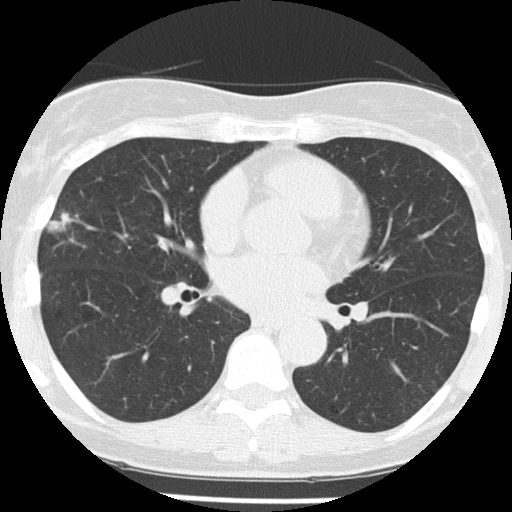
Low-dose screening chest CT, axial slice, first (baseline) screen, lung window (W 1500 / L -600 HU). Female participant, aged 58 years at enrolment. Former smoker at enrolment.
Expert reader's lesion annotation, bounding box <31,195,85,254> (left, top, right, bottom; pixels). Screening reader's record for this exam (one nodule recorded; not confirmed to be the boxed lesion): non-calcified nodule or mass ≥4 mm, right middle lobe, 18 × 9 mm, spiculated (stellate) margins, soft tissue attenuation. Later outcome: lung cancer diagnosed 79 days after this screen — non-small cell carcinoma, right middle lobe, poorly differentiated (G3), stage IA (AJCC 6th edition), 18 mm at pathology.